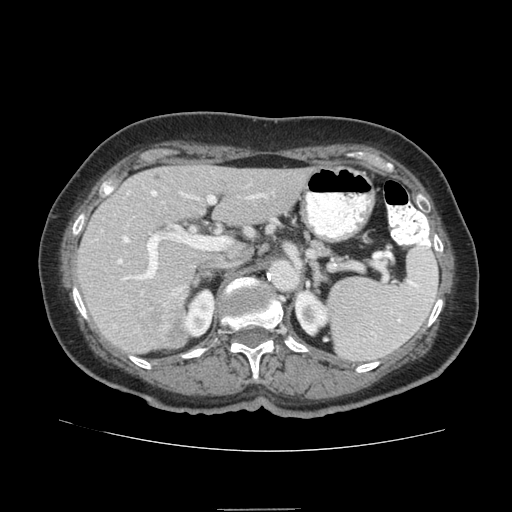
Contrast-enhanced abdominal CT (liver protocol), one axial slice. Slice 46 of 95 in the series (ordered by position). Reconstruction kernel STANDARD. Soft-tissue window (W 400 / L 40 HU). 2.5 mm slice thickness. 512 × 512 image matrix, field of view 360 × 360 mm. From the clinical record (not read from this slice): diagnosis: hepatocellular carcinoma (patient treated with transarterial chemoembolisation; whether this scan precedes or follows treatment is not stated here); TNM stage (as recorded): Stage-IVA; Child-Pugh class: B; tumour differentiation: moderately differentiated; tumour nodularity: uninodular.
Structures marked on this image (semi-automatically segmented with operator editing):
- liver parenchyma outside the tumour (the mass and vessels are separate outlines, so this box may not span the whole liver): bounding box <76,164,315,352> (left, top, right, bottom; pixels)
- mass: <139,297,188,348>
- liver vessels: <118,190,265,295>